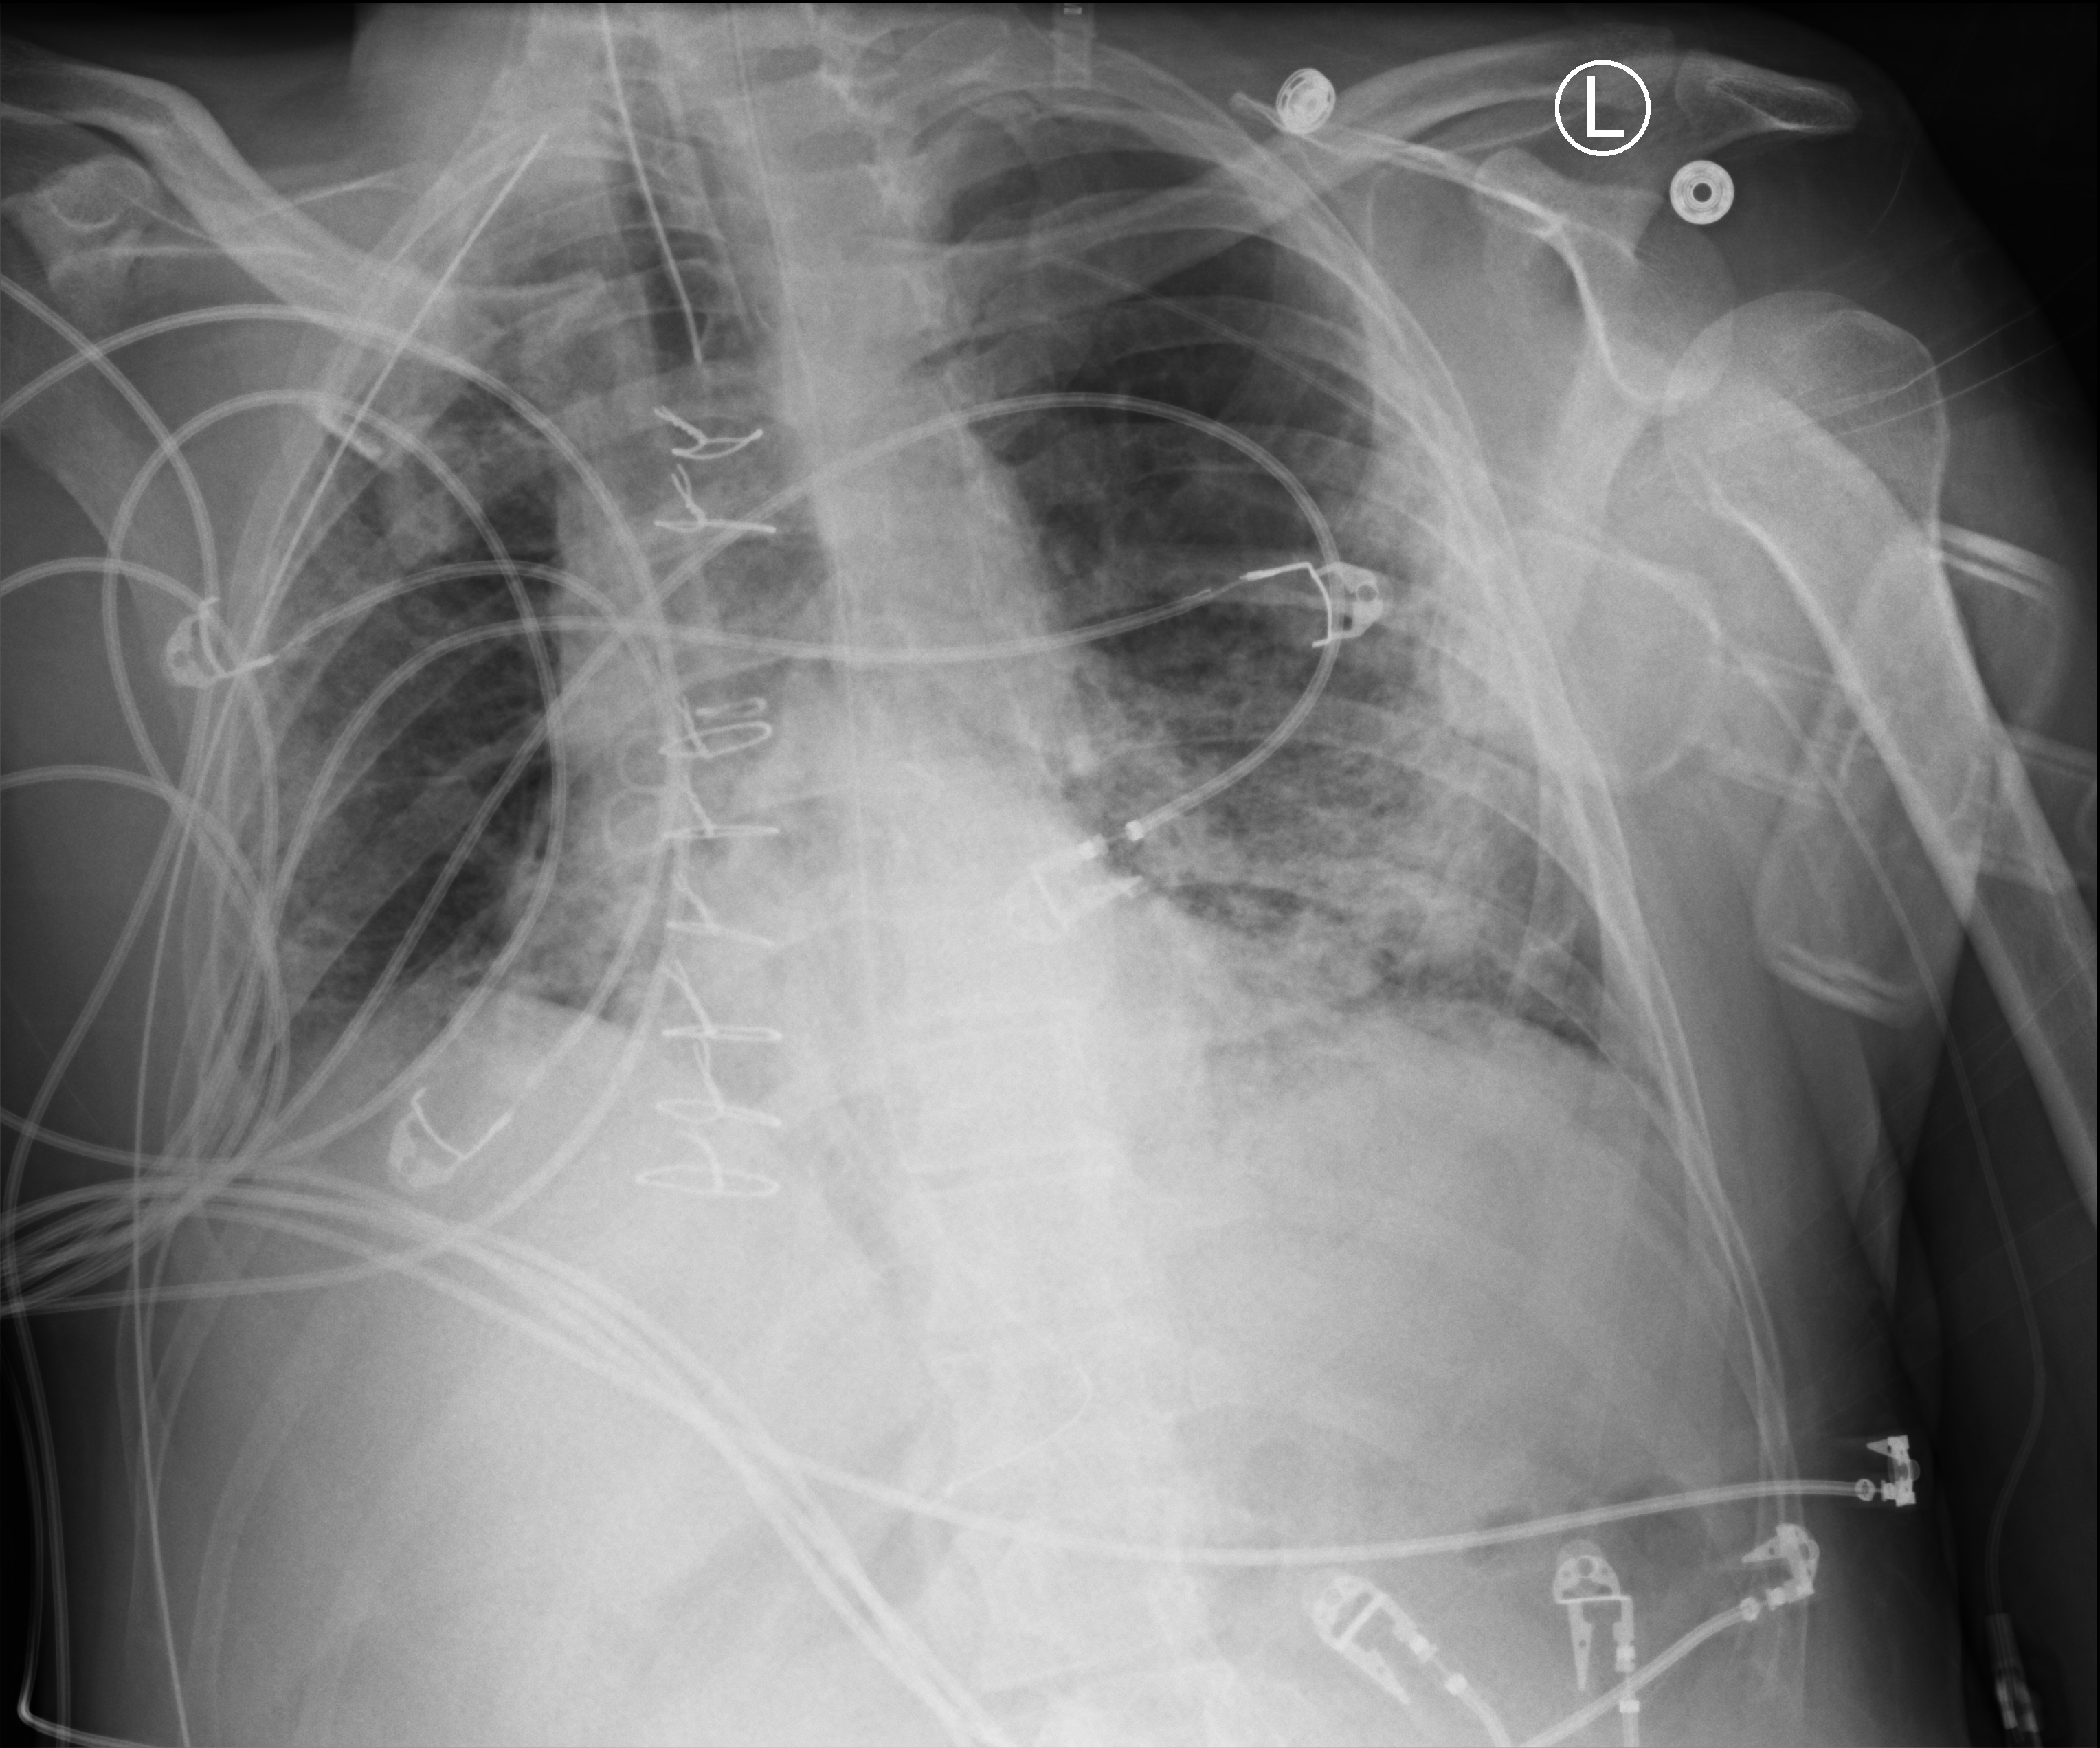
Bedside chest radiograph (computed radiography); anteroposterior (AP) projection. Male patient hospitalised with COVID-19, age 18–59 years.
Admission-level facts for this patient (not findings on this image; timing relative to this image not recorded): admitted to intensive care during this hospital stay: yes; diabetes (admission record): yes; mechanically ventilated during this hospital stay: yes.